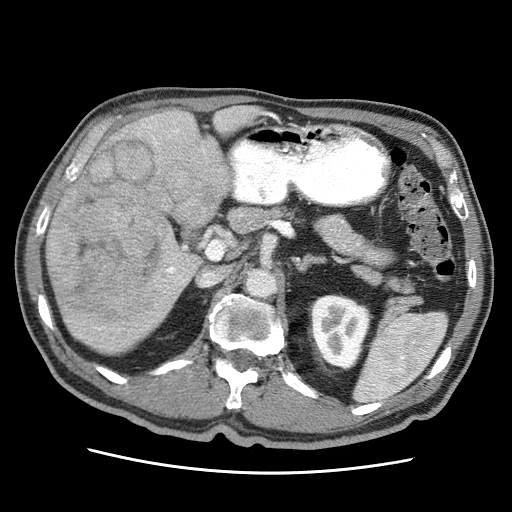
Contrast-enhanced abdominal CT (liver protocol), one axial slice; slice 22 of 75 in the series (ordered by position); reconstruction kernel STANDARD; 120 kVp; soft-tissue window (W 400 / L 40 HU); 512 × 512 image matrix, field of view 360 × 360 mm. From the clinical record (not read from this slice): diagnosis: hepatocellular carcinoma (patient treated with transarterial chemoembolisation; whether this scan precedes or follows treatment is not stated here); TNM stage (as recorded): Stage-IIIA; Child-Pugh class: A.
Annotated regions visible in this slice (semi-automatic segmentation, software-assisted and operator-edited):
- liver parenchyma outside the tumour (the mass and vessels are separate outlines, so this box may not span the whole liver): bounding box <46,106,260,353> (left, top, right, bottom; pixels)
- mass: <47,137,225,324>
- liver vessels: <98,115,220,331>